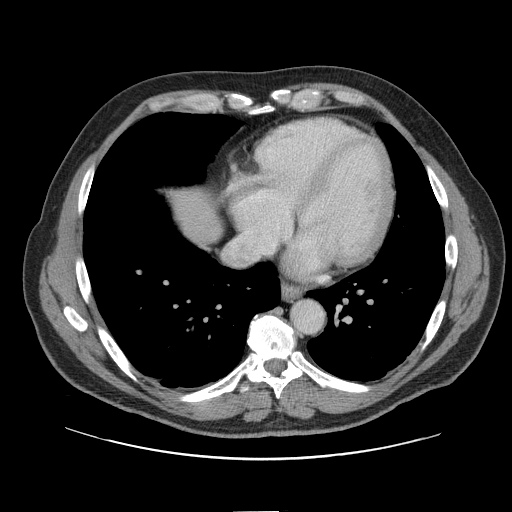
Contrast-enhanced abdominal CT, one axial slice; position 144 of 161 along the scan axis; 120 kVp; soft-tissue window (W 400 / L 40 HU); 512 × 512 image matrix, field of view 412 × 412 mm. Male patient, age 66 years. From the clinical record (not read from this slice): diagnosis: colorectal cancer liver metastases, imaged before liver resection.
Structures marked on this image (expert manual segmentation):
- liver: bounding box <175,190,220,241> (left, top, right, bottom; pixels)
- planned liver remnant (the part of the liver to remain after resection): <174,191,220,241>